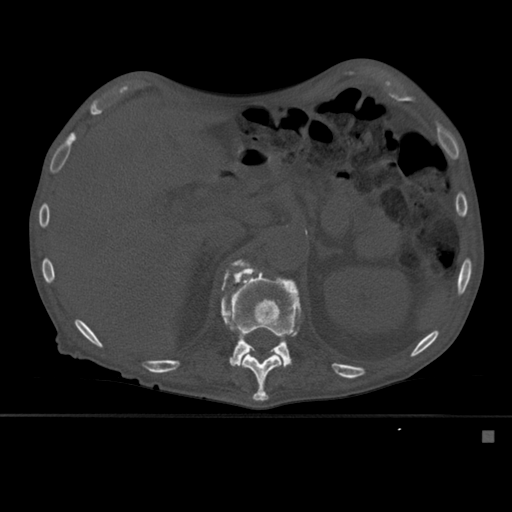
CT including the spine, one axial slice; bone window (W 1800 / L 400 HU); 1.5 mm slice thickness; 512 × 512 image matrix, field of view 373 × 373 mm. Patient: male, 78 years. From the clinical record (not read from this slice): primary cancer: prostate.
Outlined on this slice (semi-automatic segmentation, software-assisted and operator-edited):
- L1 vertebra: bounding box [x1, y1, x2, y2] px = [221, 268, 300, 398]
- T12 vertebra: [221, 259, 301, 401]